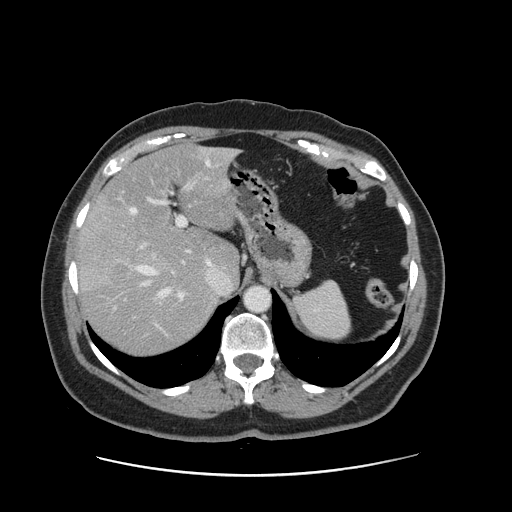
Contrast-enhanced abdominal CT, one axial slice. Position 108 of 161 along the scan axis. Intravenous contrast given. Soft-tissue window (W 400 / L 40 HU). 2.5 mm slice thickness. 512 × 512 image matrix, field of view 398 × 398 mm. Female patient, age 62 years. Case-level facts recorded for this patient, not image findings: diagnosis: colorectal cancer liver metastases, imaged before liver resection; multiple liver metastases: no; largest metastasis: 2.5 cm; disease in both lobes: no.
Structures marked on this image (outlined manually by an expert reader):
- hepatic veins: bounding box [x1, y1, x2, y2] px = [130, 161, 229, 296]
- liver: [80, 146, 239, 355]
- planned liver remnant (the part of the liver to remain after resection): [100, 147, 238, 278]
- portal vein (with intrahepatic branches): [113, 172, 203, 310]
- liver metastasis: [108, 264, 131, 290]